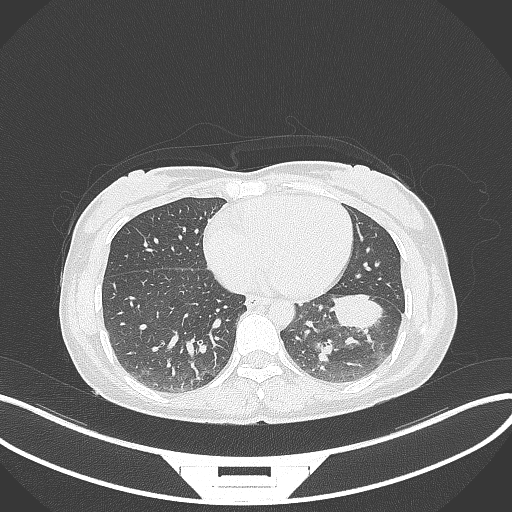
Chest CT, one axial slice. Position 15 of 244 along the scan axis. Reconstruction kernel B70f. 120 kVp. Lung window (W 1500 / L -600 HU). 512 × 512 image matrix, field of view 400 × 400 mm. Patient: female, 41 years. Case-level facts recorded for this patient, not image findings: clinical TNM (as recorded): T2a N3 M1b.
Outlined on this slice (rectangle marked by the reading radiologist):
- lung tumour (recorded histology: adenocarcinoma): box from (x=331, y=291) to (x=387, y=336) px